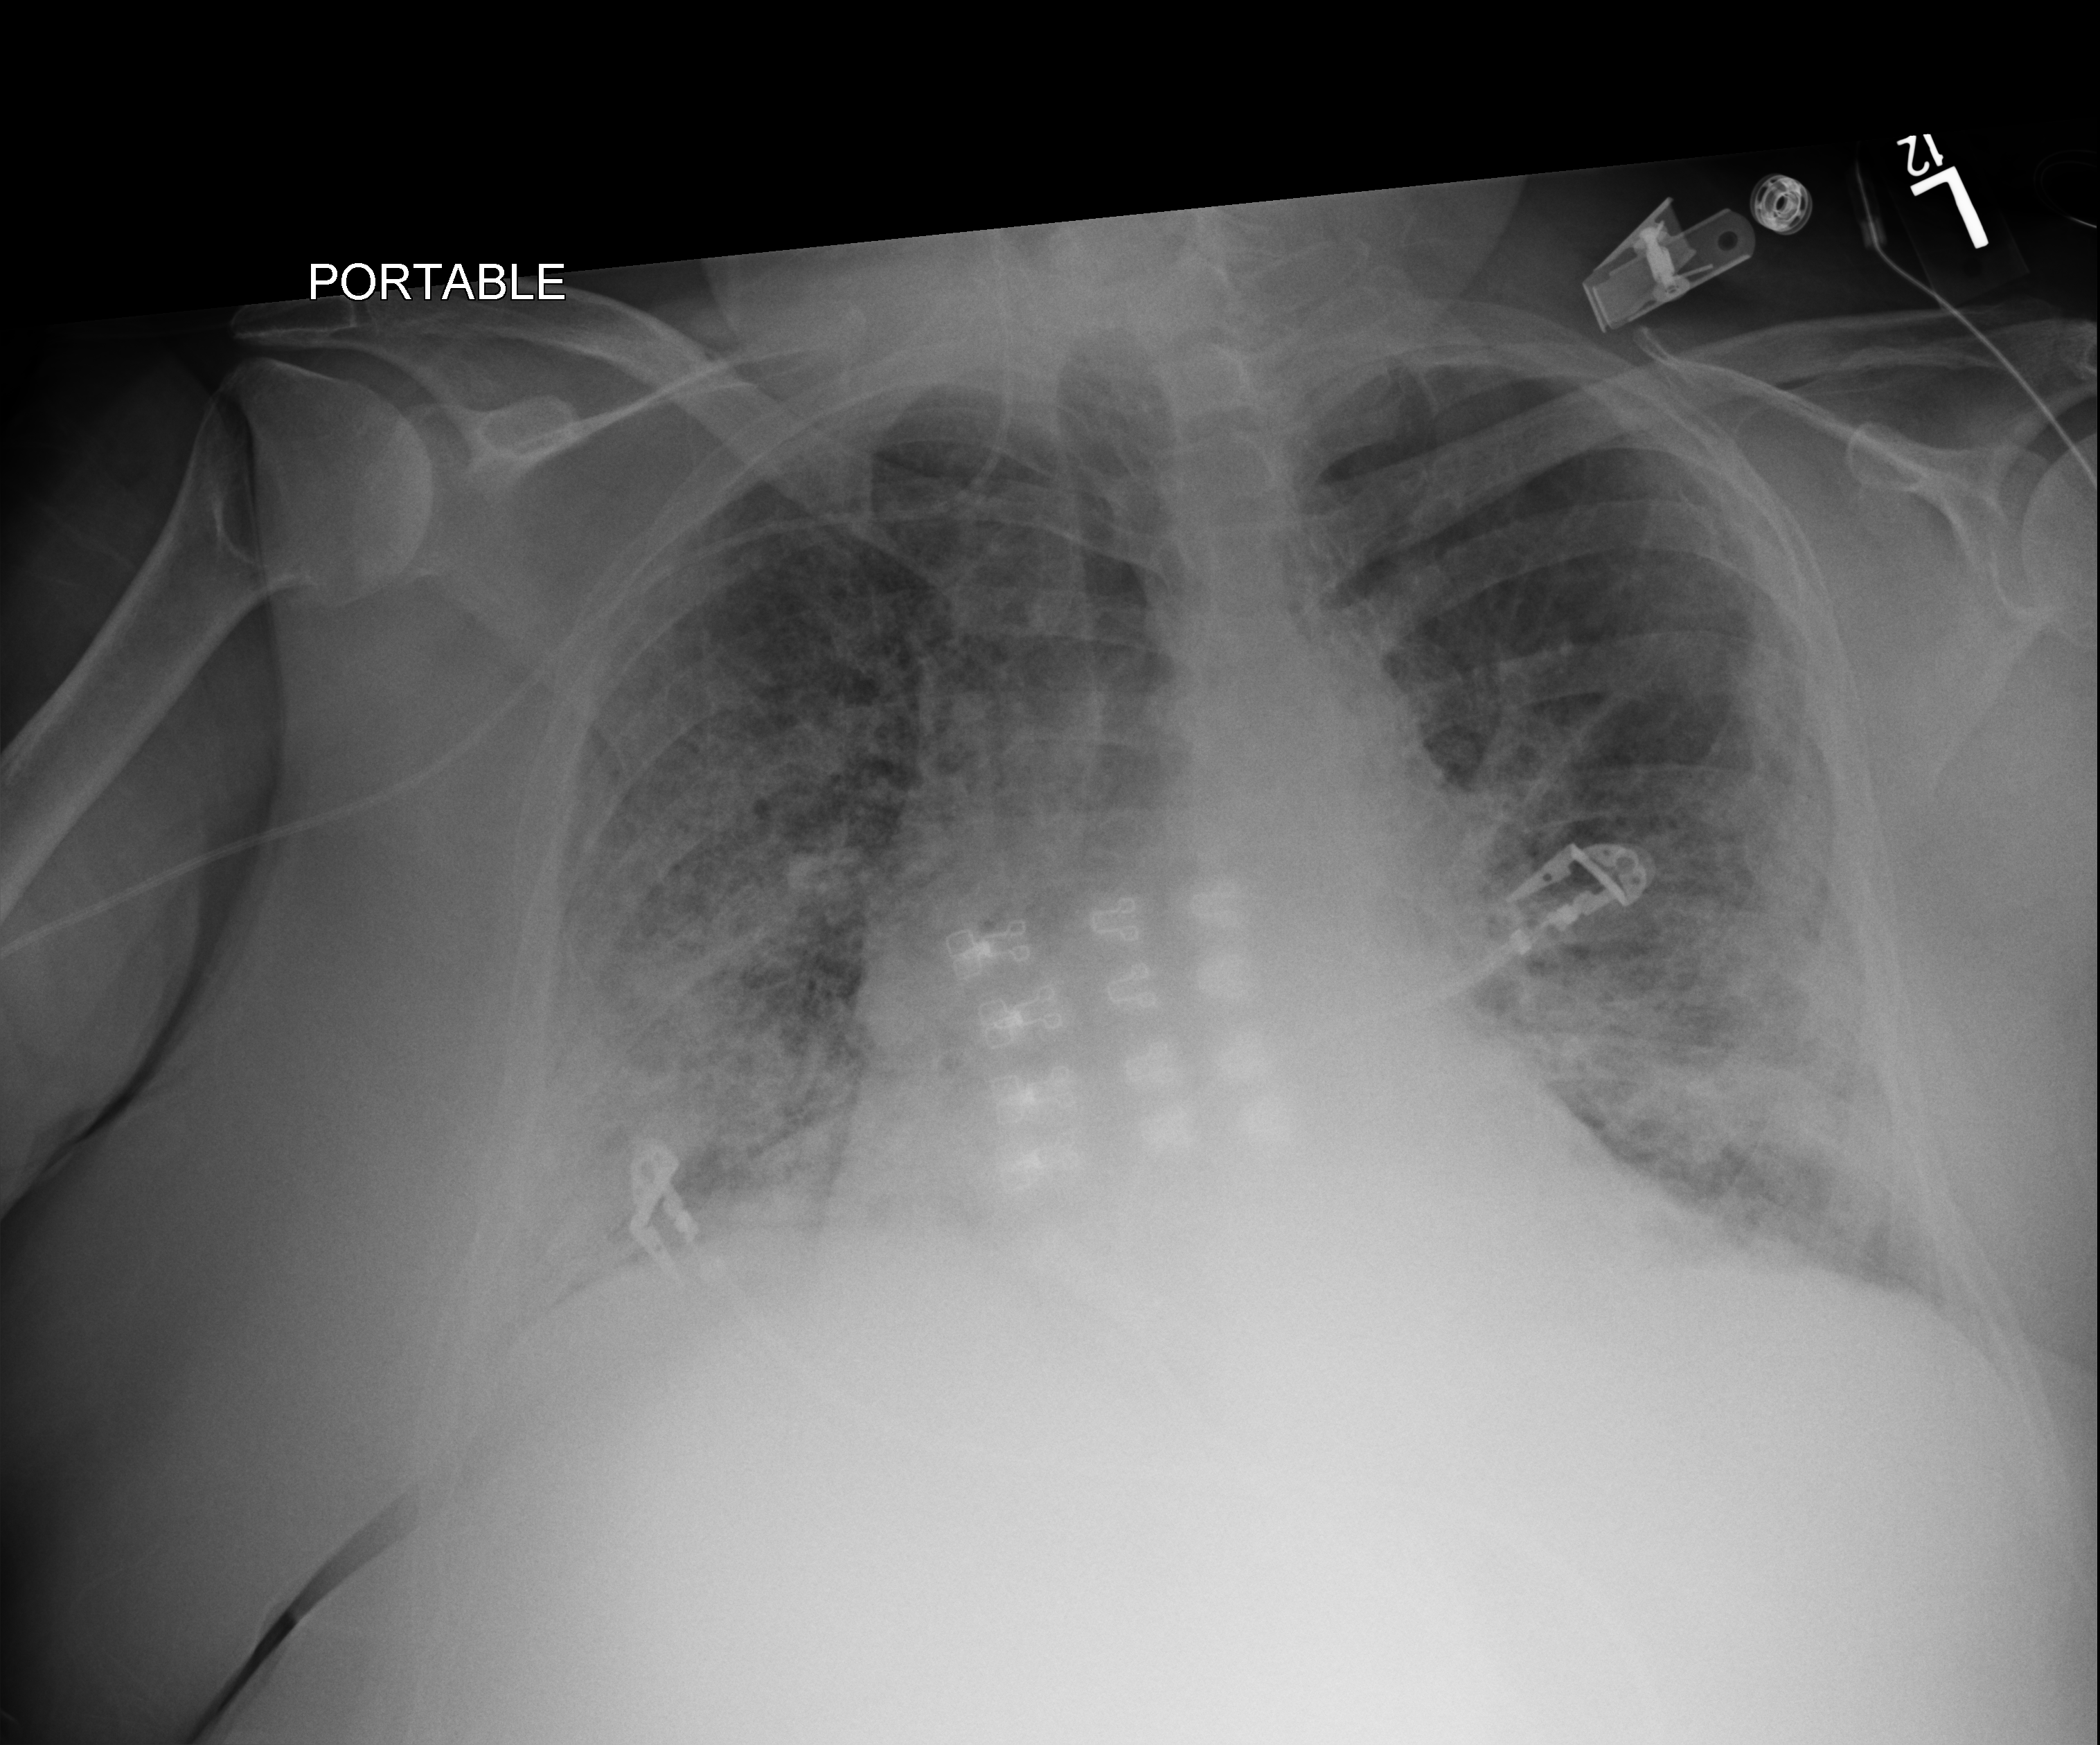
Chest X-ray (portable); anteroposterior (AP) projection. Female patient hospitalised with COVID-19, age 60–74 years.
Hospital-stay facts (about this admission, not read from this image; timing relative to this image not recorded):
- admitted to intensive care during this hospital stay: yes